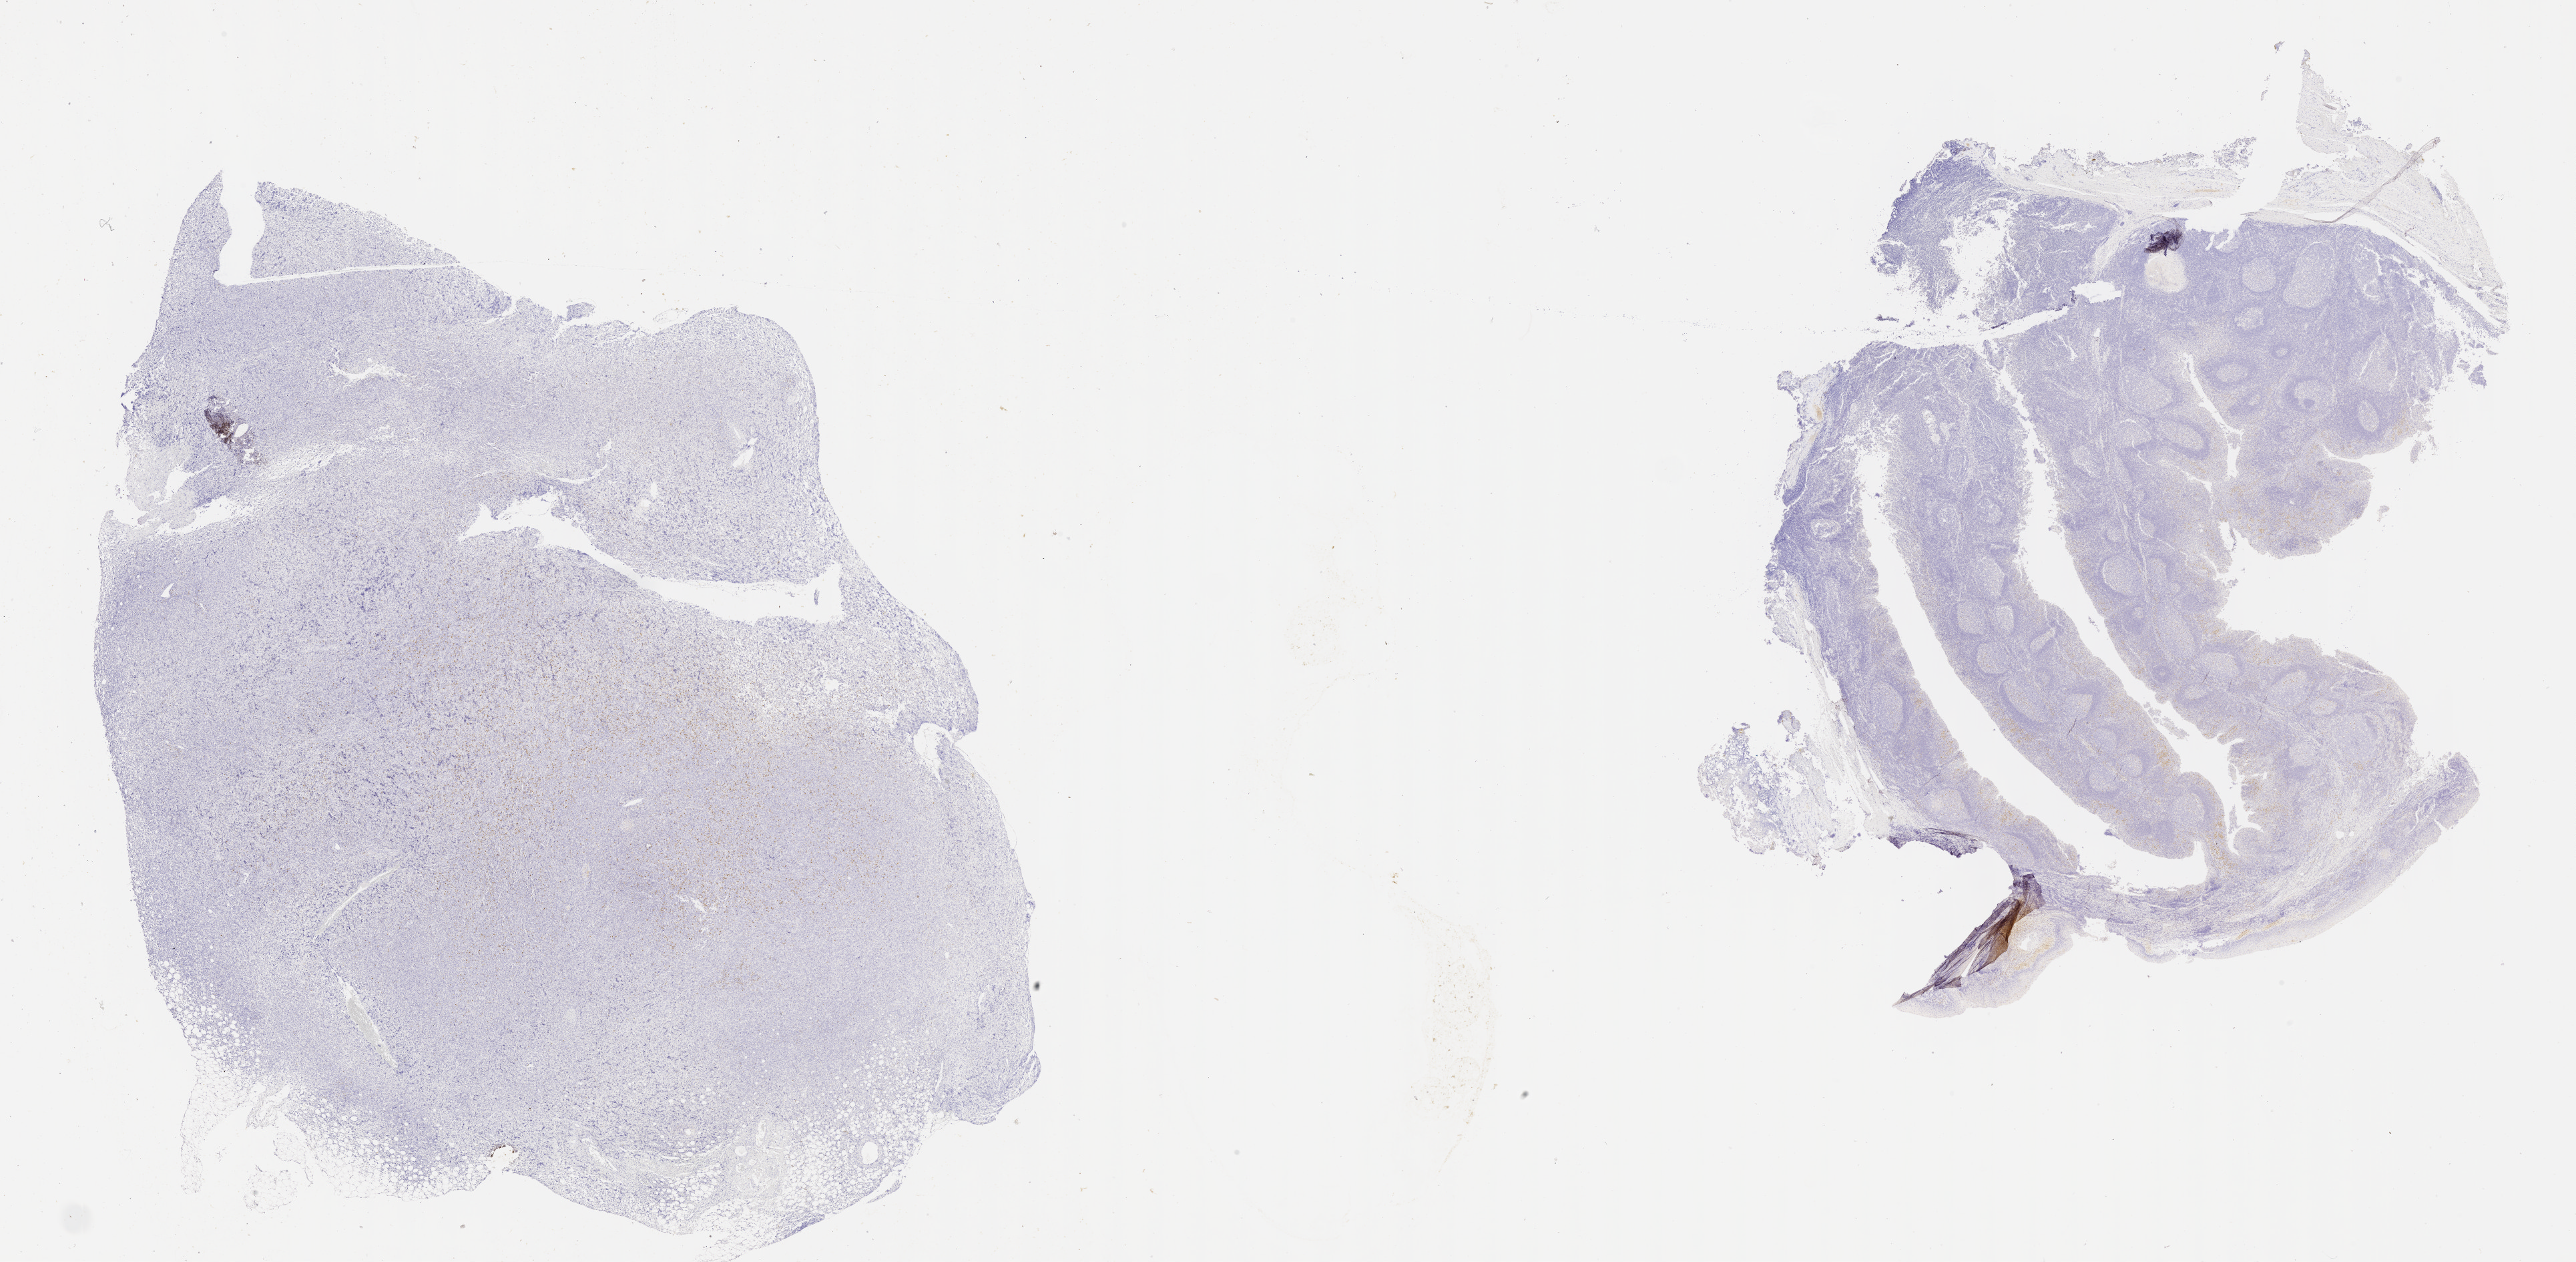
Immunohistochemistry (IHC) whole-slide image stained for IRF4/MUM1 — whole scanned area (about 31.2 x 15.3 mm) shown as a low-resolution overview. Patient sex: female.
* specimen: tumor tissue